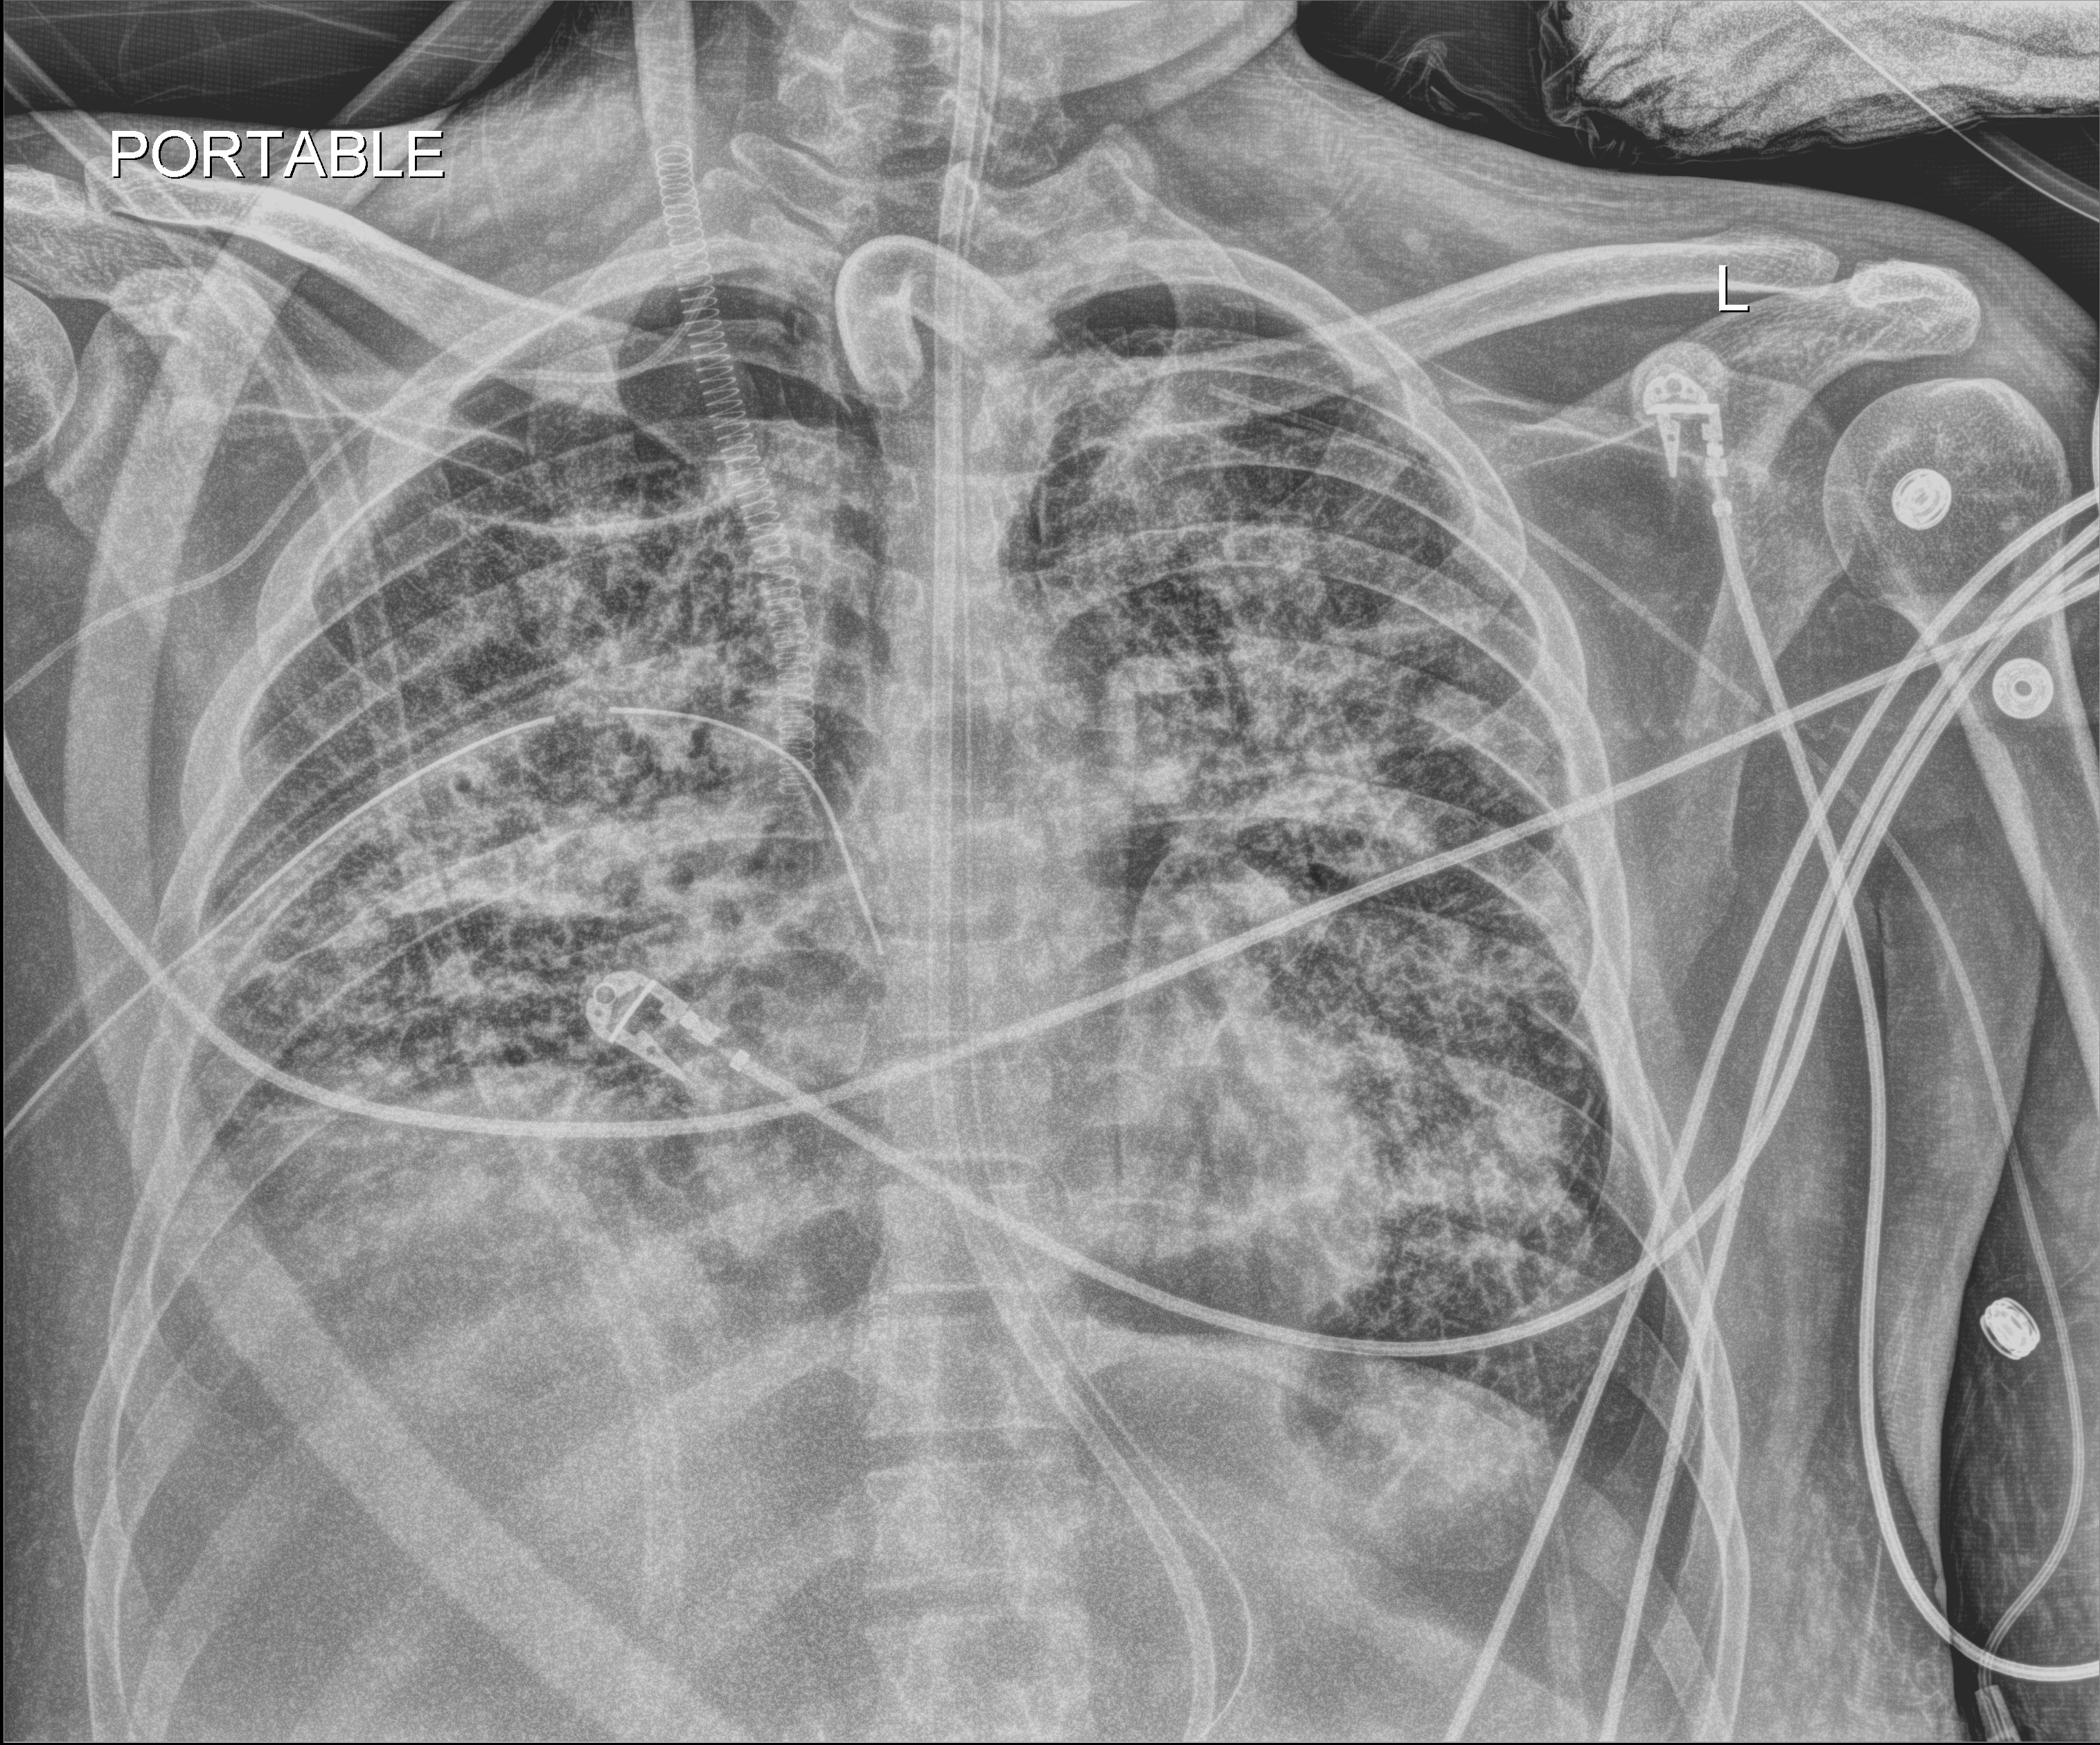
Portable chest radiograph. Adult patient hospitalised with COVID-19, age 18–59 years.
Admission-level facts for this patient (not findings on this image; timing relative to this image not recorded): smoking status (admission record): never.